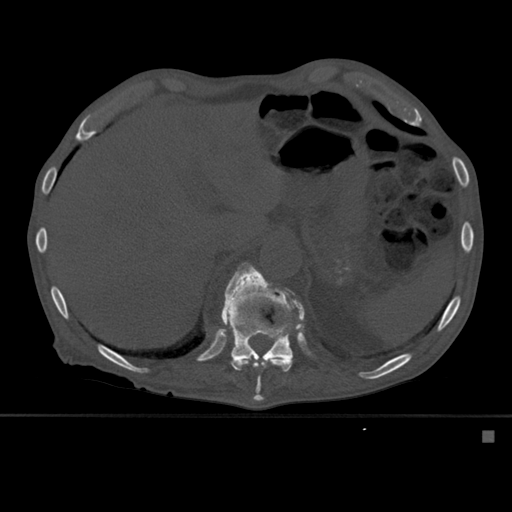
CT including the spine, one axial slice. Bone window (W 1800 / L 400 HU). 1.5 mm slice thickness. 512 × 512 image matrix, field of view 373 × 373 mm. Patient: male, 78 years. From the clinical record (not read from this slice): primary cancer: prostate.
Structures marked on this image (semi-automatically segmented with operator editing):
- T11 vertebra: bounding box (x1, y1, x2, y2) in pixels: (231, 262, 300, 401)
- T12 vertebra: (221, 273, 305, 359)